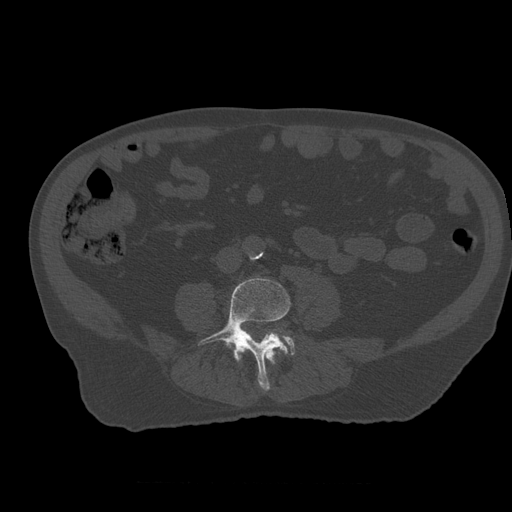
CT including the spine, one axial slice; position 164 of 399 along the scan axis; reconstruction kernel STANDARD; 120 kVp; bone window (W 1800 / L 400 HU); 1.25 mm slice thickness; 512 × 512 image matrix. Patient age 73 years. Case-level facts recorded for this patient, not image findings: primary cancer: prostate.
Annotated regions visible in this slice (semi-automatically segmented with operator editing):
- L3 vertebra: bounding box <239,350,276,364> (left, top, right, bottom; pixels)
- L4 vertebra: <199,278,291,390>
- L5 vertebra: <284,337,295,355>